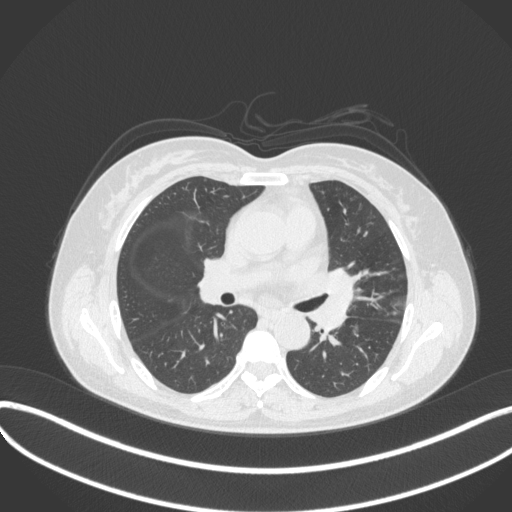
Chest CT, one axial slice. Position 196 of 373 along the scan axis. Reconstruction kernel B31f. 120 kVp. Lung window (W 1500 / L -600 HU). 1 mm slice thickness. 512 × 512 image matrix. Female patient, age 54 years. From the clinical record (not read from this slice): clinical TNM (as recorded): T2a N1 M0; histopathological grade: G3.
Structures marked on this image (bounding box drawn by a radiologist):
- lung tumour (recorded histology: small cell carcinoma): box from (x=315, y=266) to (x=358, y=336) px